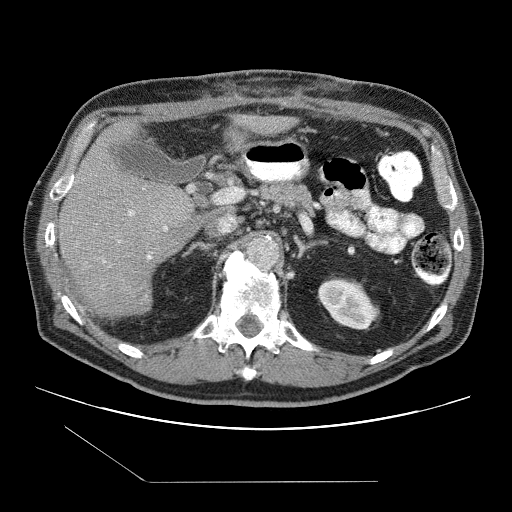
Contrast-enhanced abdominal CT (liver protocol), one axial slice. Slice 52 of 109 in the series (ordered by position). 120 kVp. One of 2 acquisitions stored at this slice position. Soft-tissue window (W 400 / L 40 HU). 512 × 512 image matrix, field of view 400 × 400 mm. From the clinical record (not read from this slice): diagnosis: hepatocellular carcinoma (patient treated with transarterial chemoembolisation; whether this scan precedes or follows treatment is not stated here); TNM stage (as recorded): Stage-IIIB; Child-Pugh class: A; tumour differentiation: well differentiated.
Outlined on this slice (semi-automatically segmented with operator editing):
- liver parenchyma outside the tumour (the mass and vessels are separate outlines, so this box may not span the whole liver): bounding box (x1, y1, x2, y2) in pixels: (56, 116, 295, 314)
- liver vessels: (103, 210, 168, 263)